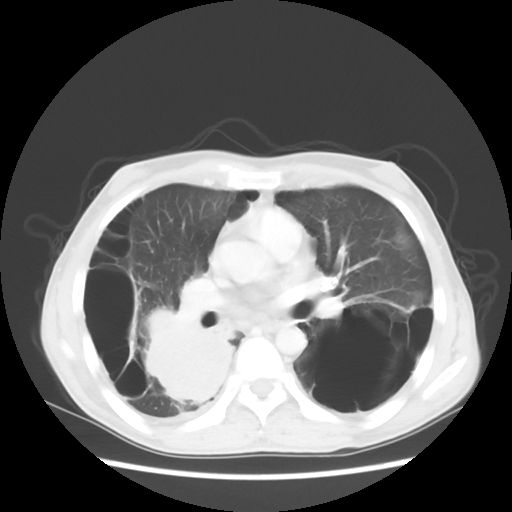
Chest CT, one axial slice; slice 29 of 56 in the series (ordered by position); lung window (W 1500 / L -600 HU); 5 mm slice thickness; 512 × 512 image matrix, field of view 351 × 351 mm. Male patient, age 41 years. From the clinical record (not read from this slice): clinical TNM (as recorded): T4 N0 M1a; histopathological grade: G3.
Structures marked on this image (bounding box drawn by a radiologist):
- lung tumour (recorded histology: large cell carcinoma): bounding box (x1, y1, x2, y2) in pixels: (139, 303, 265, 436)